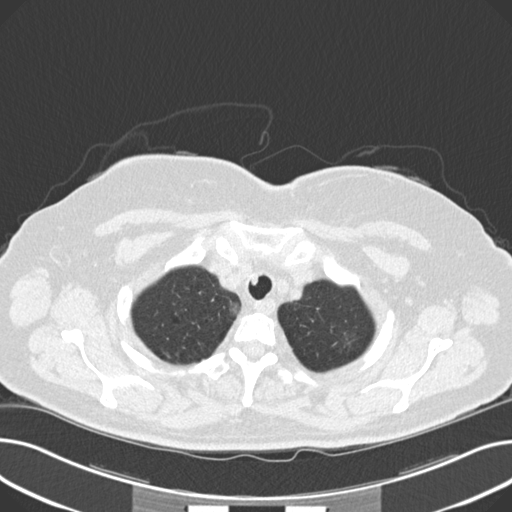
Axial slice from a low-dose chest CT screening exam; third annual screen; lung window (W 1500 / L -600 HU); 2 mm slice thickness; standard (soft-tissue) reconstruction kernel (B30f); 120 kVp; 512 × 512 image matrix, field of view 372 × 372 mm. Female, age 60 years at enrolment. Current smoker at enrolment.
Expert reader's lesion annotation, bounding box <329,325,375,362> (left, top, right, bottom; pixels). The screening reader recorded 8 non-calcified nodules or masses ≥4 mm on this exam (right upper lobe, lingula, lingula, right middle lobe, right lower lobe, left lower lobe, left lower lobe, left lower lobe); which of them this box marks is not recorded. Lung cancer was diagnosed 176 days after this screen: non-small cell carcinoma, left upper lobe, poorly differentiated (G3), stage IB (AJCC 6th edition), 7 mm at pathology.